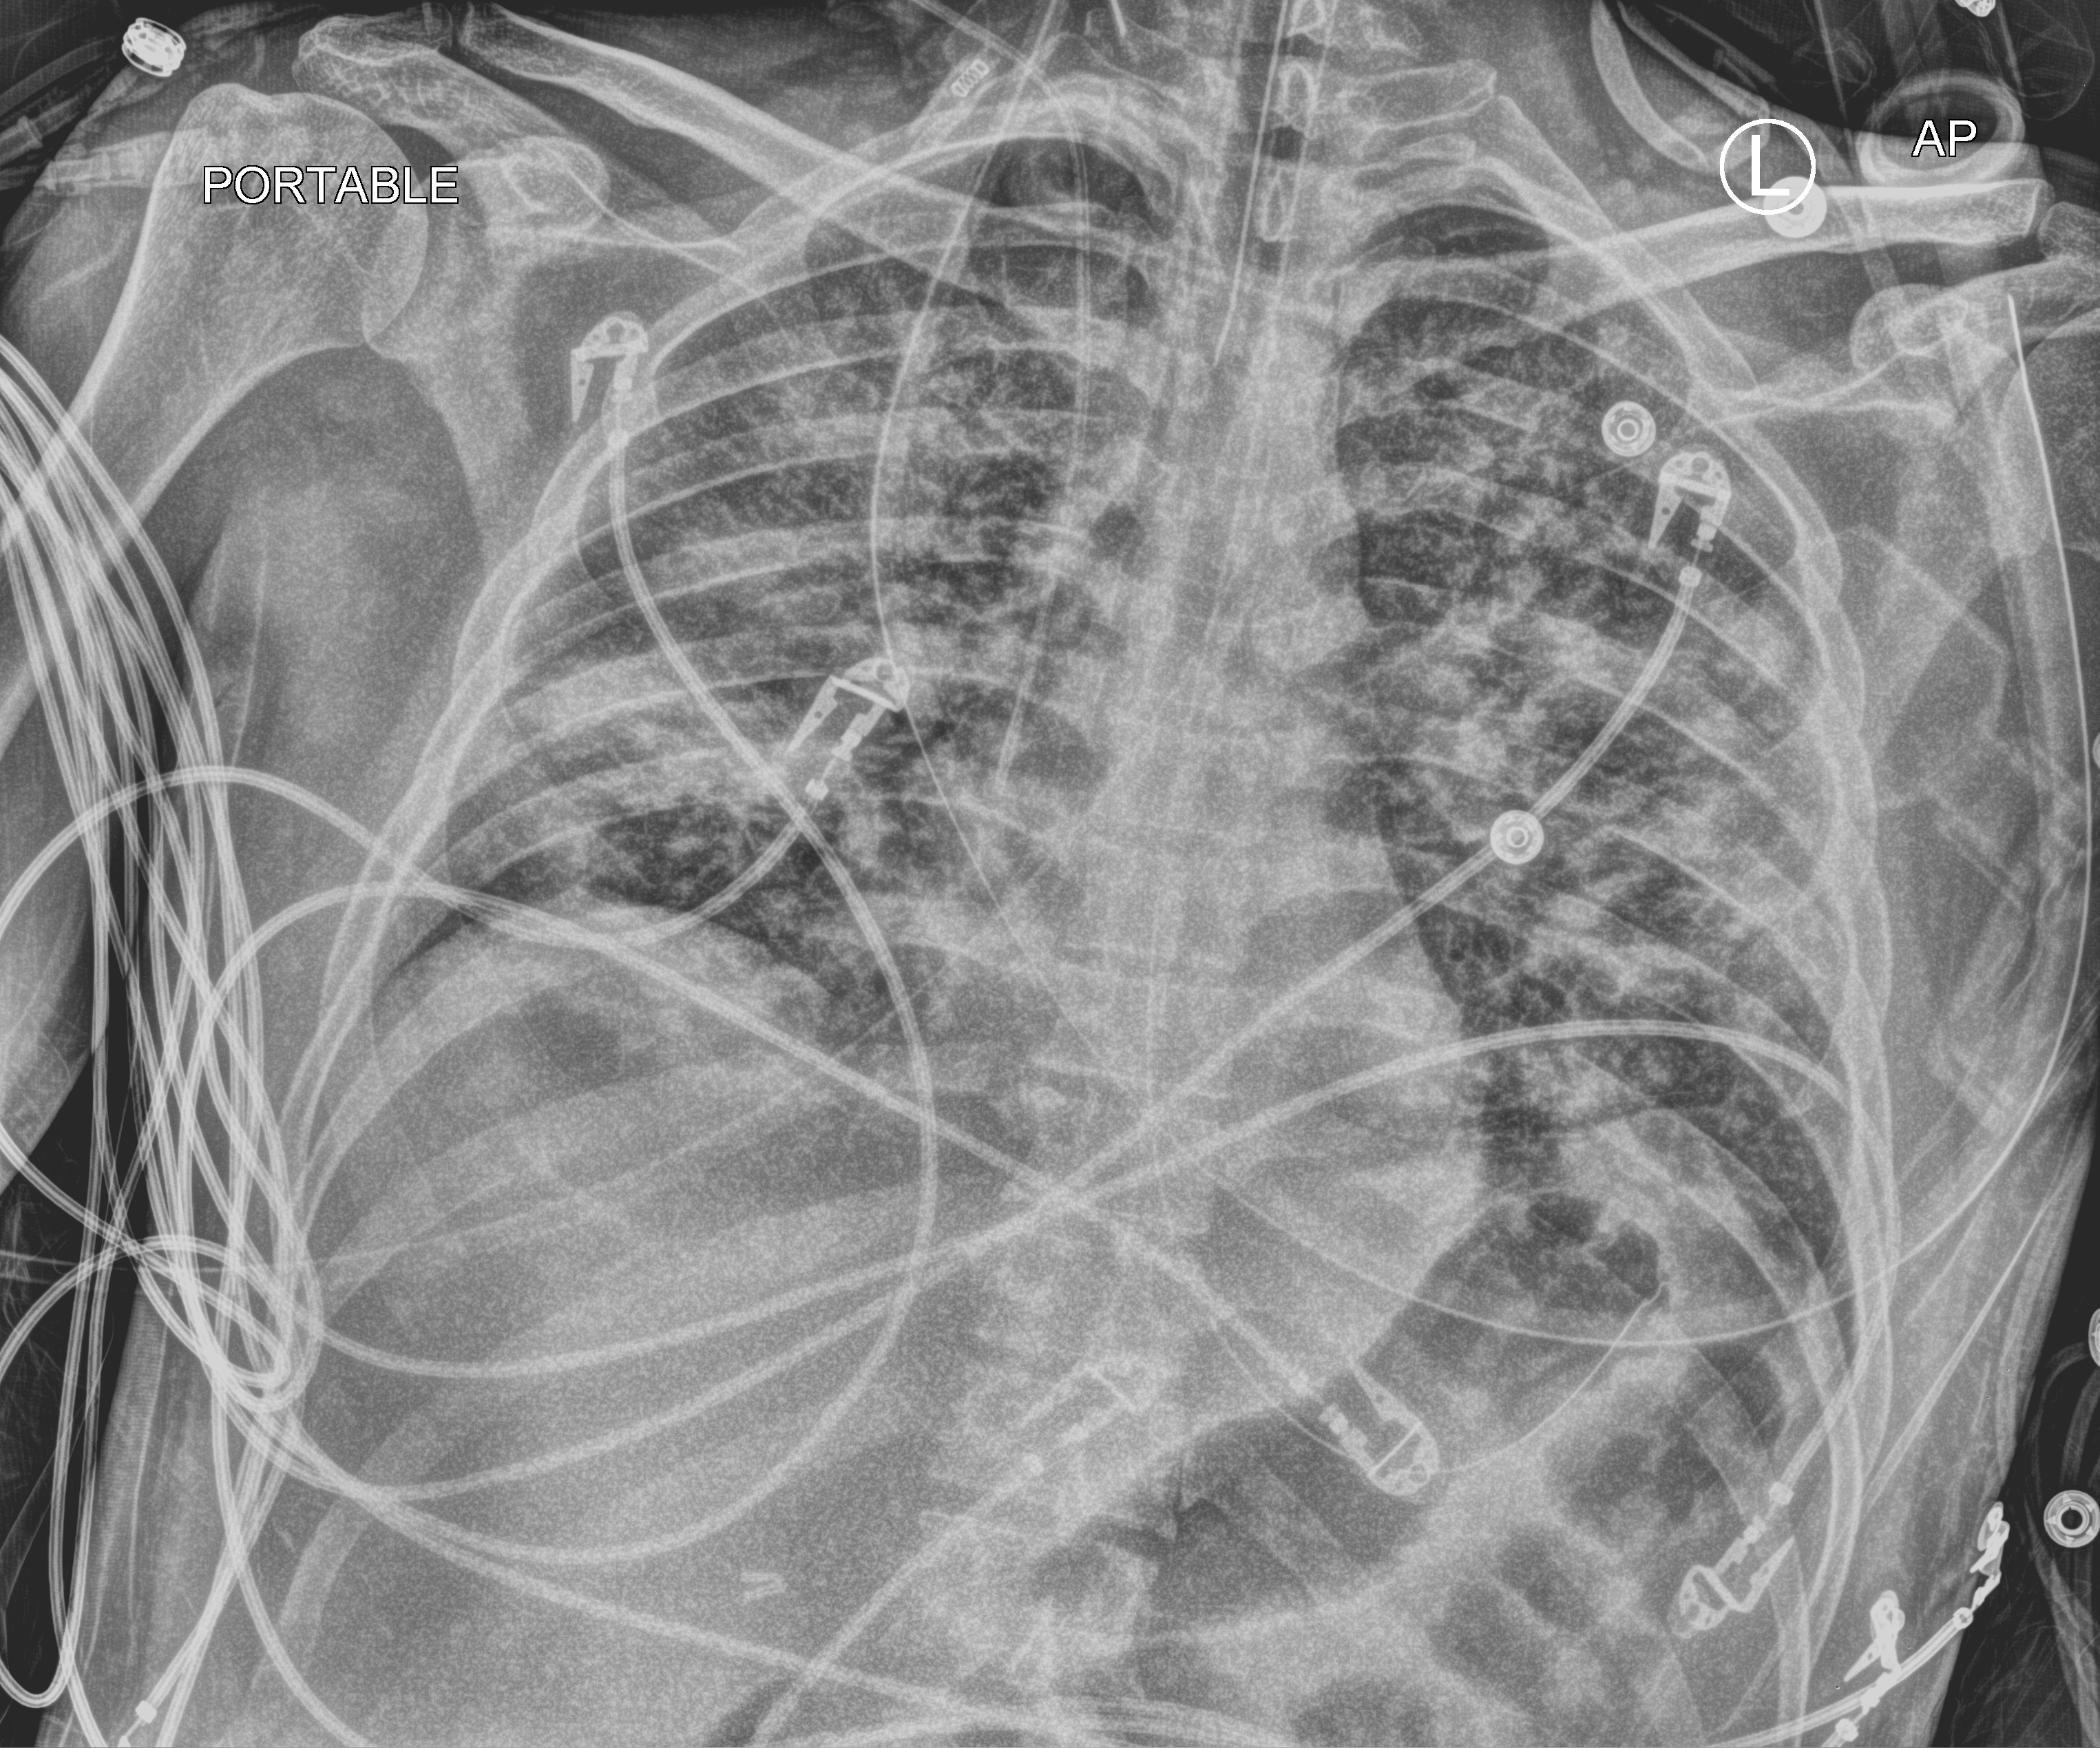
Chest X-ray (portable); anteroposterior (AP) projection. Patient hospitalised with COVID-19; male, aged 18–59 years.
From the hospital-stay record, not from the radiograph (when in the stay this image was taken is not recorded): admitted to intensive care during this hospital stay: yes; COPD (admission record): no; mechanically ventilated during this hospital stay: yes.